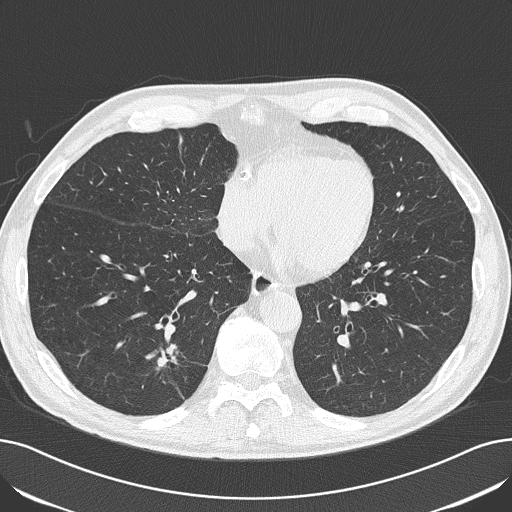
Chest CT (low-dose screening protocol), one axial image; first (baseline) screen; lung window (W 1500 / L -600 HU); slice 120 of 182 in the series; 512 × 512 image matrix. Male, age 71 years at enrolment. Current smoker at enrolment.
Expert-annotated lung lesion, bounding box (x1, y1, x2, y2) in pixels: (135, 328, 199, 387). Screening reader's record for this exam (one nodule recorded; not confirmed to be the boxed lesion): non-calcified nodule or mass ≥4 mm, right lower lobe, 14 × 14 mm, spiculated (stellate) margins, soft tissue attenuation. Participant outcome: lung cancer diagnosed 145 days after this screen — adenocarcinoma, NOS, right lower lobe, moderately differentiated (G2), stage IA (AJCC 6th edition), 24 mm at pathology.